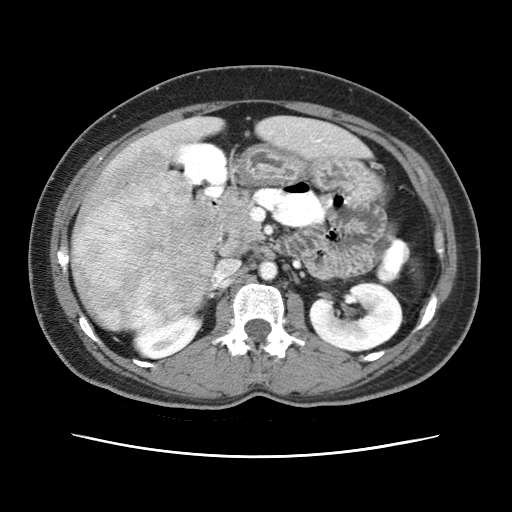
Contrast-enhanced abdominal CT (liver protocol), one axial slice. Slice 17 of 79 in the series (ordered by position). Reconstruction kernel STANDARD. 120 kVp. Soft-tissue window (W 400 / L 40 HU). 512 × 512 image matrix, field of view 340 × 340 mm. From the clinical record (not read from this slice): diagnosis: hepatocellular carcinoma (patient treated with transarterial chemoembolisation; whether this scan precedes or follows treatment is not stated here); TNM stage (as recorded): Stage-I; Child-Pugh class: A; tumour differentiation: moderately differentiated; tumour nodularity: uninodular.
Annotated regions visible in this slice (semi-automatic segmentation, software-assisted and operator-edited):
- abdominal aorta: bounding box <259,260,277,278> (left, top, right, bottom; pixels)
- liver parenchyma outside the tumour (the mass and vessels are separate outlines, so this box may not span the whole liver): <72,116,364,330>
- mass: <73,148,216,330>
- liver vessels: <317,140,321,142>